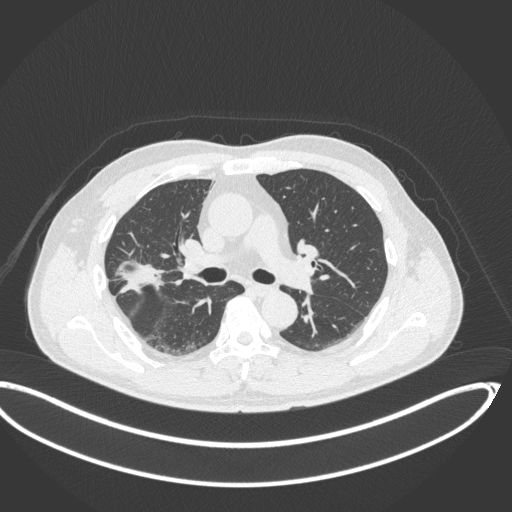
Chest CT, one axial slice. 120 kVp. Lung window (W 1500 / L -600 HU). 1 mm slice thickness. 512 × 512 image matrix, field of view 439 × 439 mm. Male patient, age 63 years. From the clinical record (not read from this slice): clinical TNM (as recorded): T1c N0 M0.
Structures marked on this image (bounding box drawn by a radiologist):
- lung tumour (recorded histology: adenocarcinoma): bounding box (x1, y1, x2, y2) in pixels: (113, 256, 169, 296)